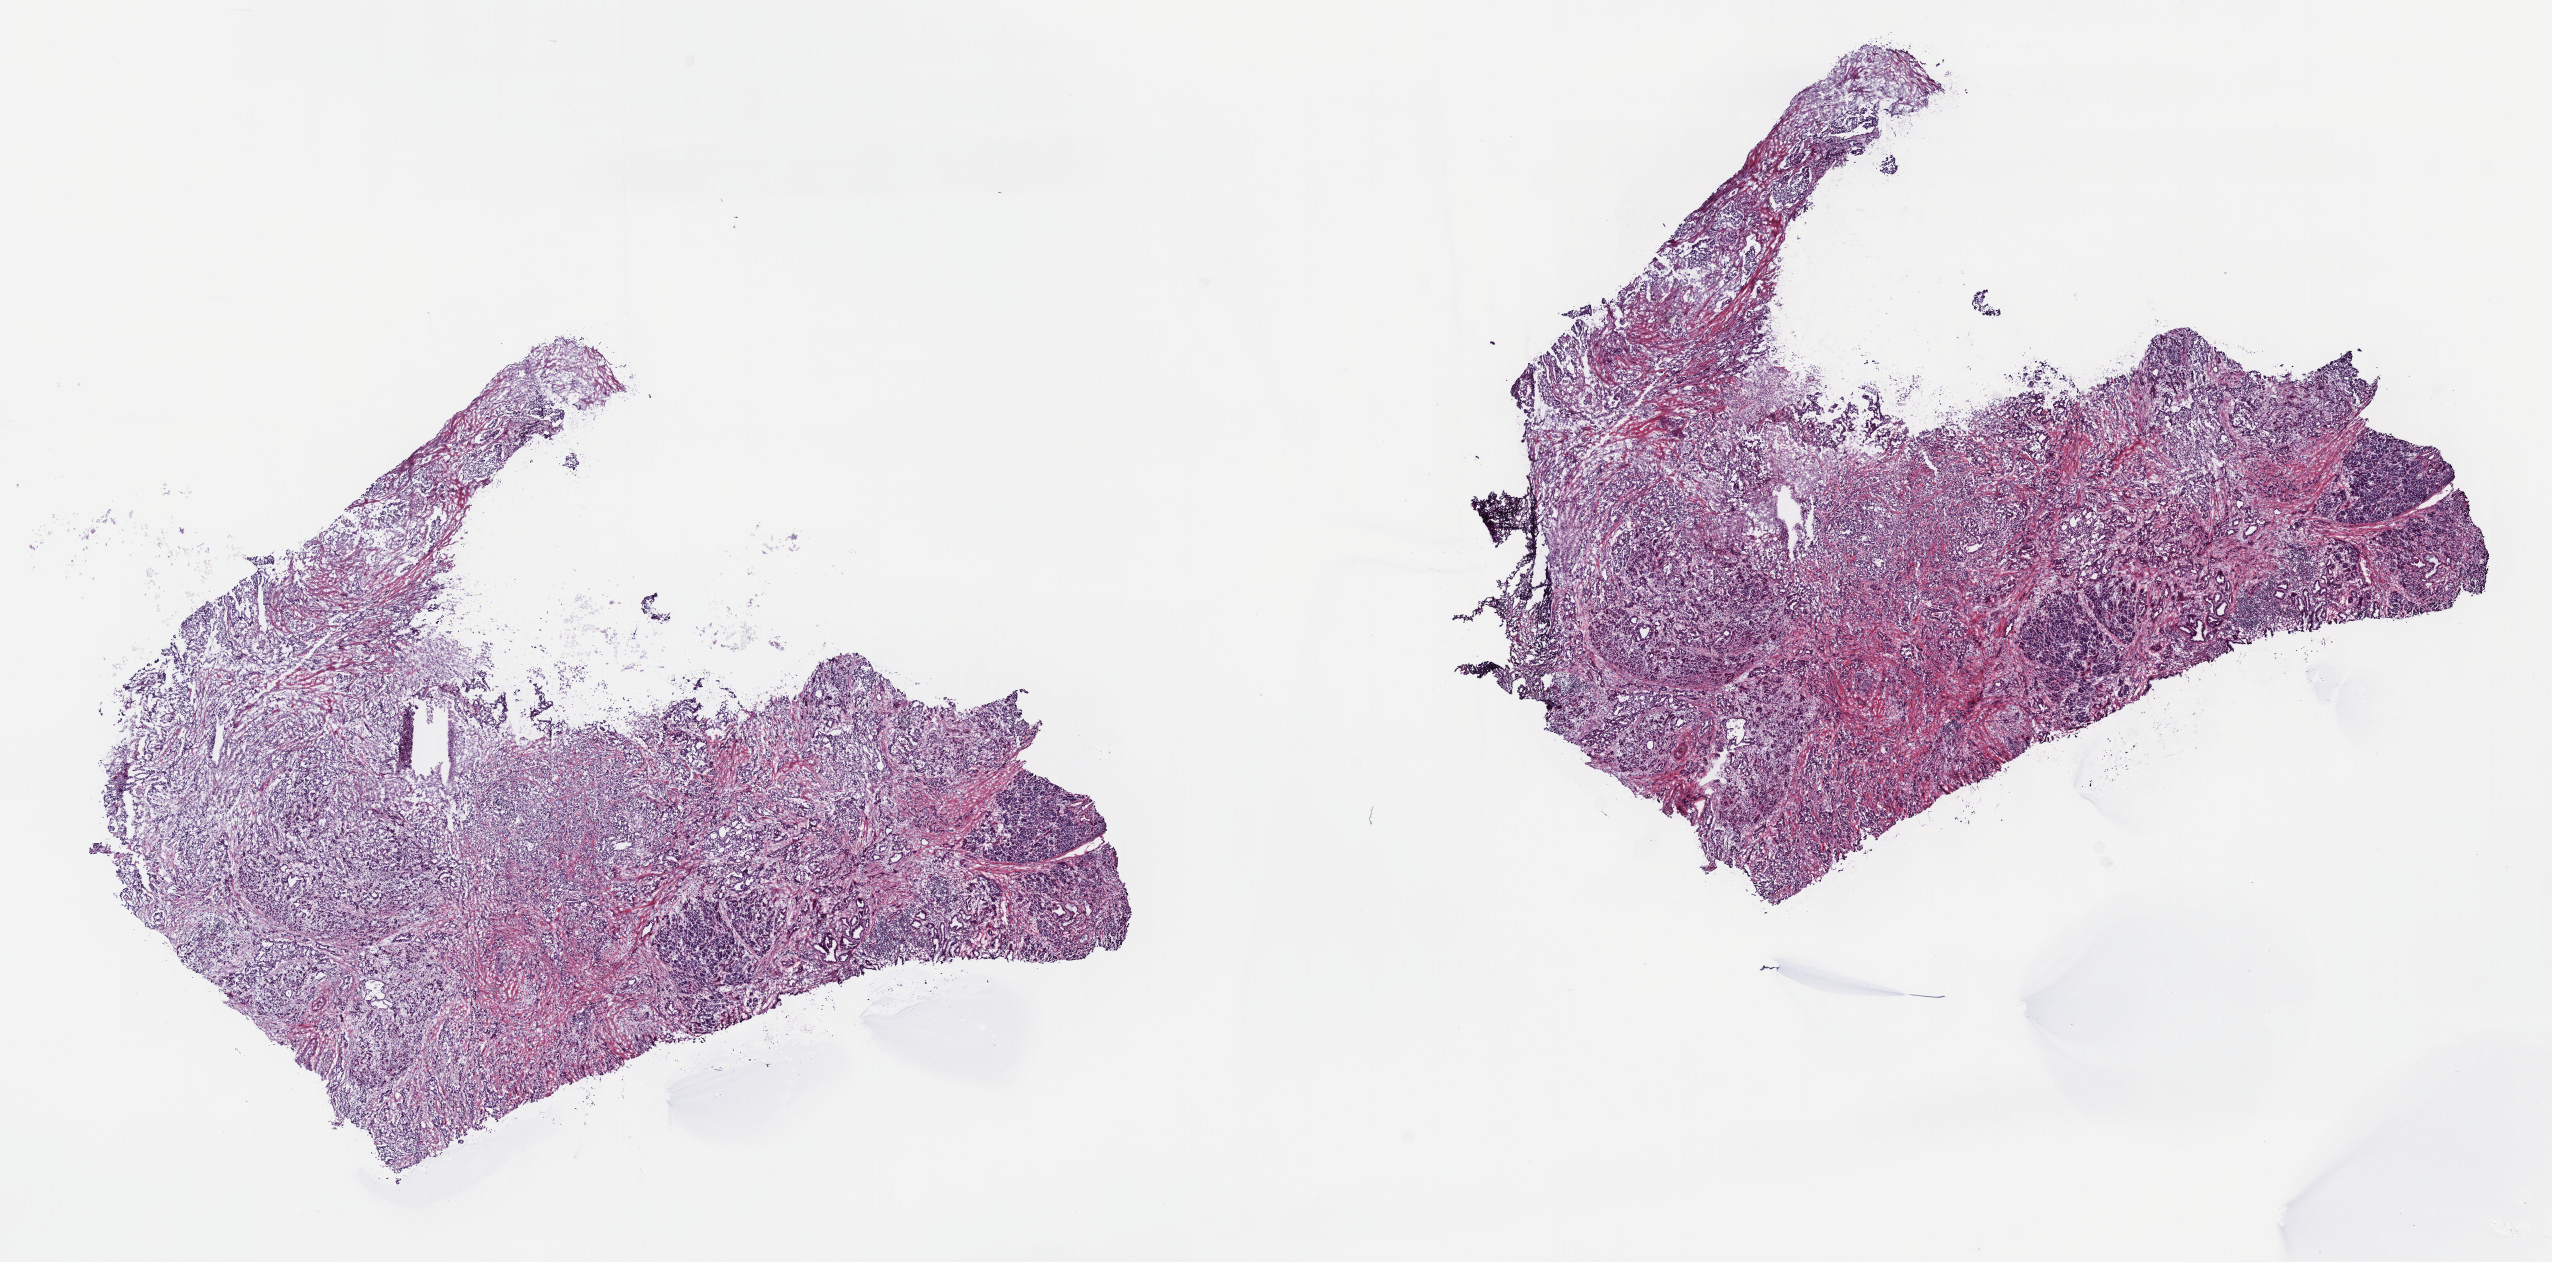
Digitized Hematoxylin and eosin (H&E) stained tissue section (whole slide), low-resolution overview of the scanned area, about 20.6 x 10.2 mm; frozen section from the top of the tissue portion; sample: primary tumour, pancreas. Male, age 65 years at initial diagnosis. Histologic grade: G3 (poorly differentiated). Pathologist review of this section (percent, as recorded): tumour cells 80%, tumour nuclei 60%, normal cells 20%, stromal cells 0%, necrosis 0%. Inflammatory infiltration, as recorded: lymphocyte infiltration 0%, monocyte infiltration 0%, neutrophil infiltration 0%.
TNM: T3 N1 MX. Diagnosis: Infiltrating duct carcinoma, NOS (head of pancreas). AJCC pathologic stage: IIB (7th edition). Lymph nodes positive (case pathology): 2 of 25 examined.